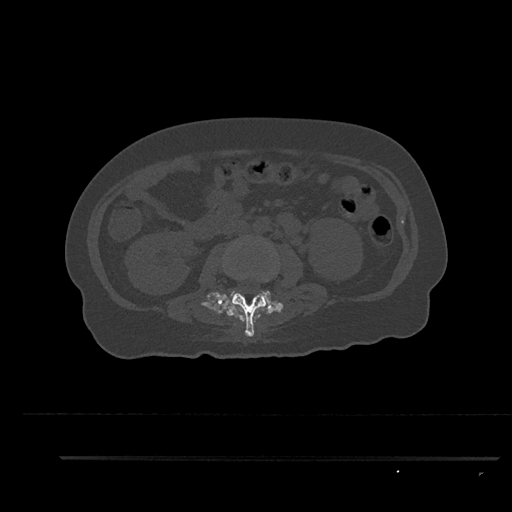
CT including the spine, one axial slice; 120 kVp; bone window (W 1800 / L 400 HU); 0.5 mm slice thickness; 512 × 512 image matrix. Female patient, age 44 years. Case-level facts recorded for this patient, not image findings: primary cancer: renal; vertebrae with lytic lesions (as recorded): L1.
Structures marked on this image (semi-automatic segmentation, software-assisted and operator-edited):
- L2 vertebra: bounding box (x1, y1, x2, y2) in pixels: (225, 268, 268, 337)
- L3 vertebra: (224, 290, 277, 307)